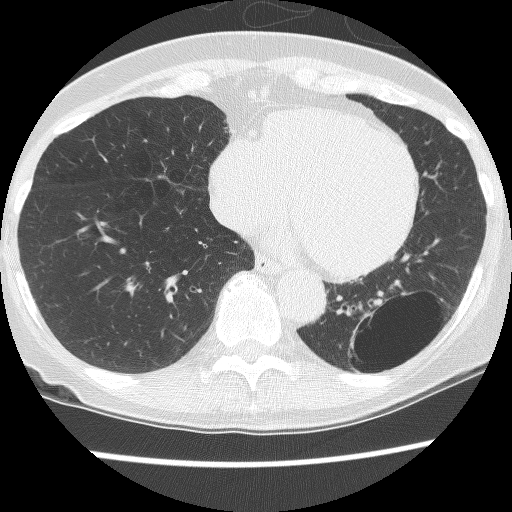
Chest CT (low-dose screening protocol), one axial image; third screening round (two years after baseline); lung window (W 1500 / L -600 HU); slice 89 of 130 in the series; 512 × 512 image matrix. Female, age 61 years at enrolment. Current smoker at enrolment.
Expert-annotated lung lesion, bounding box [x1, y1, x2, y2] px = [332, 291, 447, 388]. The screening reader recorded 2 non-calcified nodules or masses ≥4 mm on this exam; which of them this box marks is not recorded. Official screen result: positive, no significant change: stable abnormalities potentially related to lung cancer, unchanged since the prior screening exam. Lung cancer was diagnosed 166 days after this screen: non-small cell carcinoma, left lower lobe, poorly differentiated (G3), stage IB (AJCC 6th edition), 100 mm at pathology.